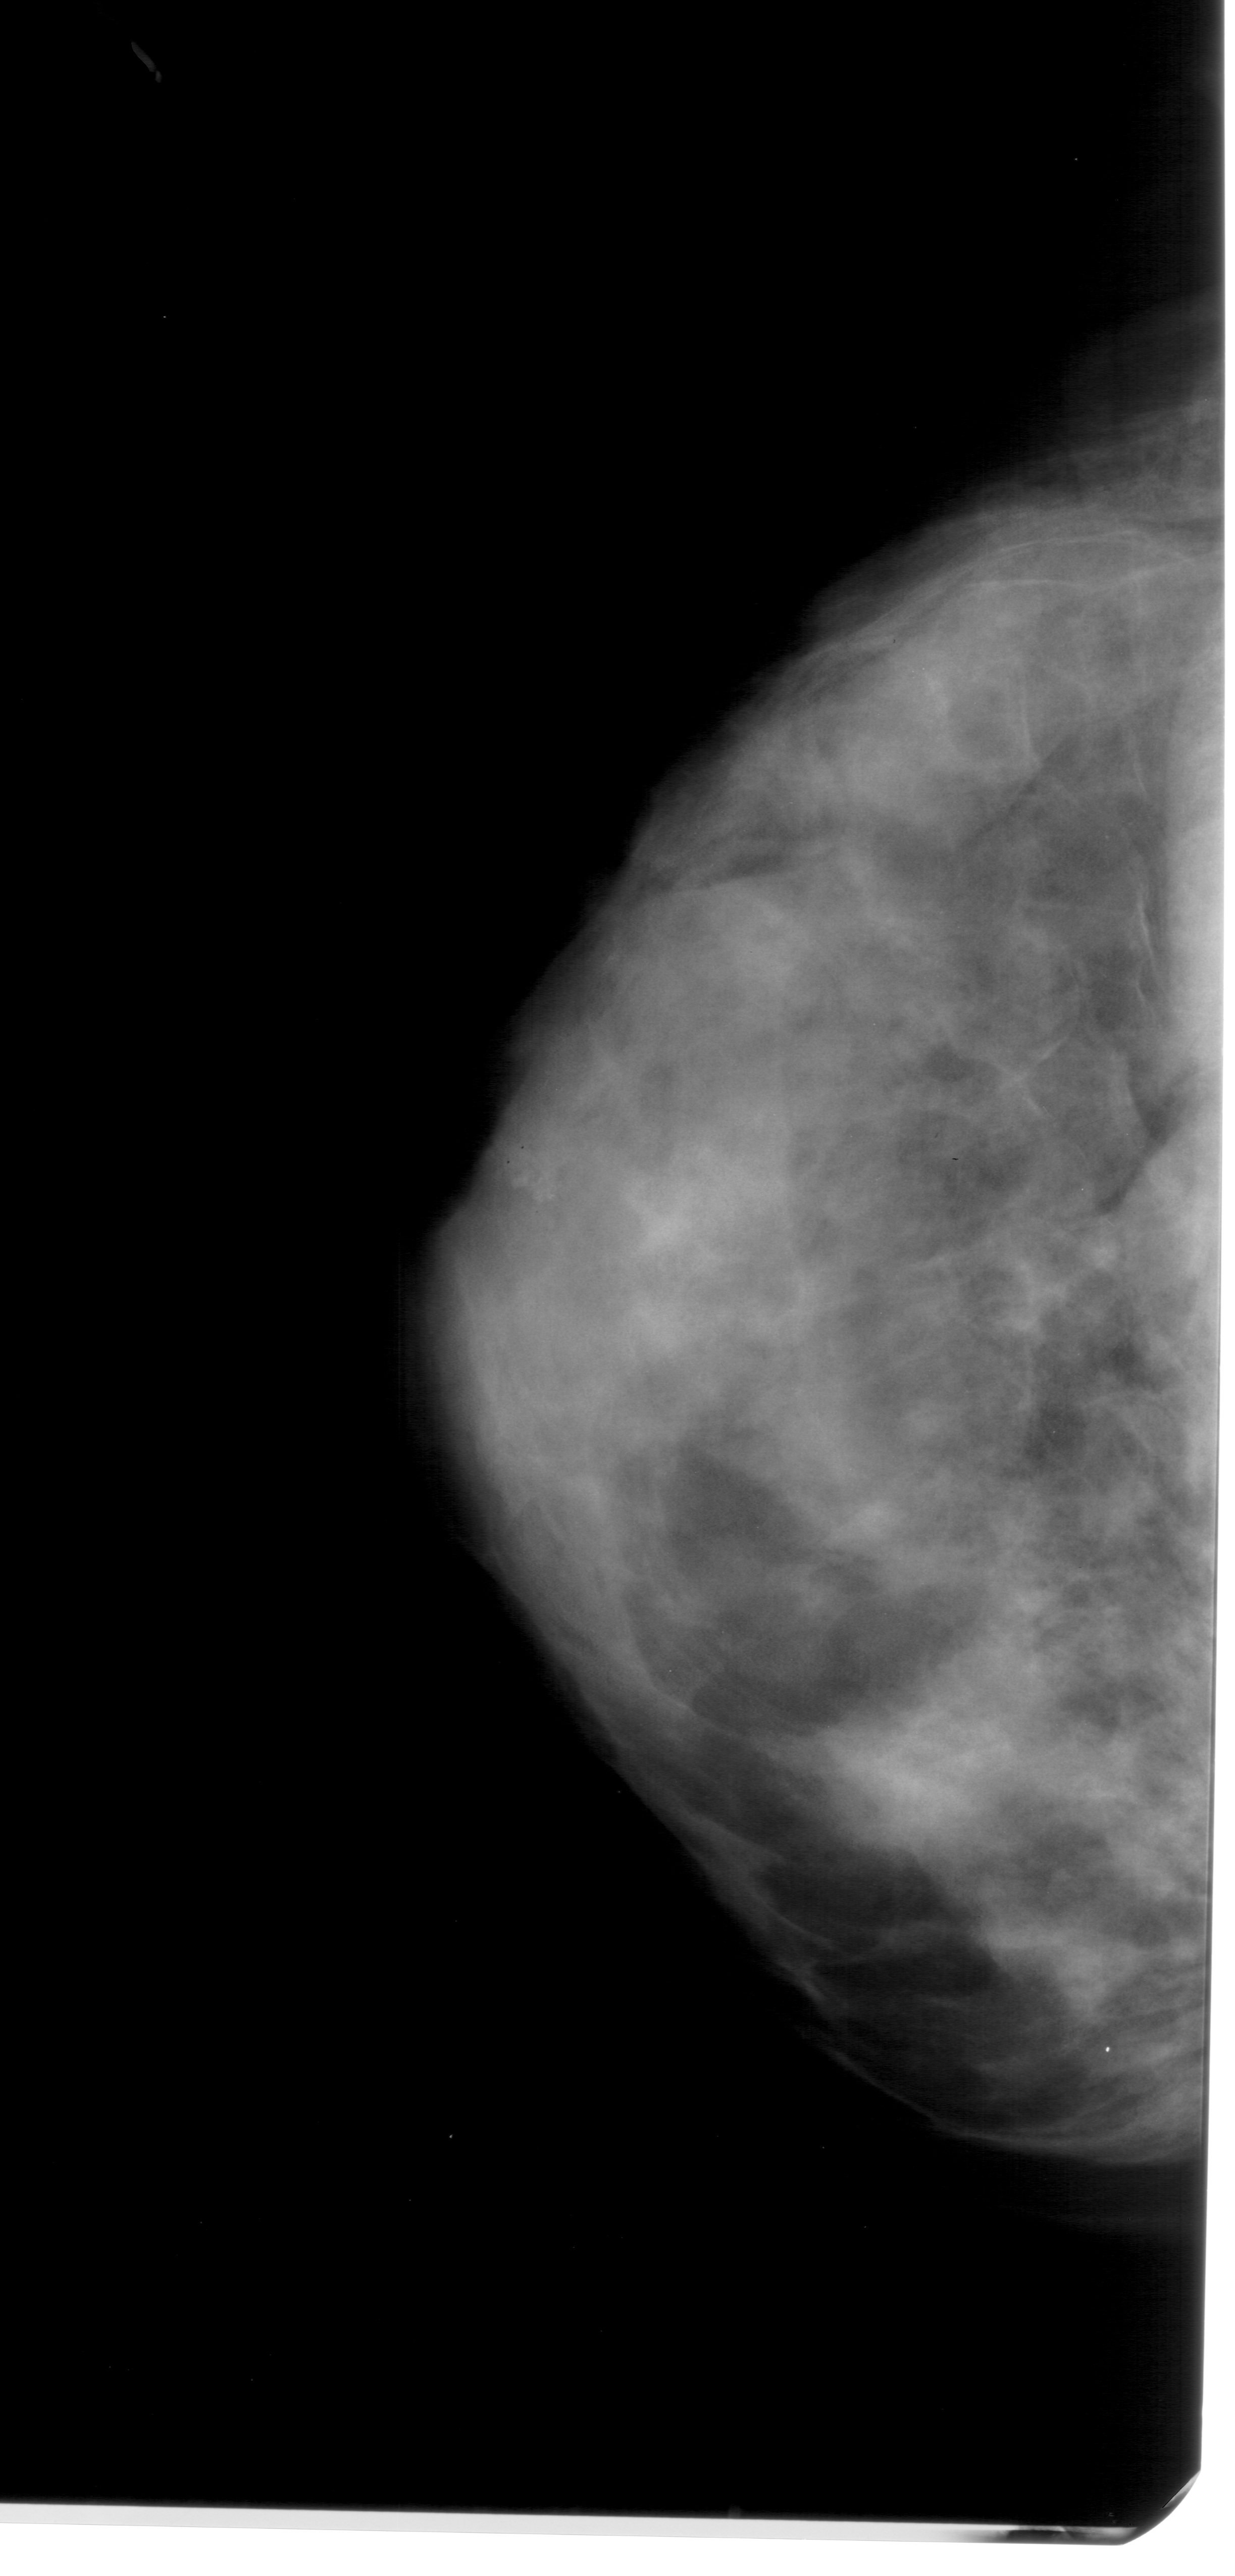
Scanned film-screen mammogram; left breast; CC view; breast composition: extremely dense (BI-RADS density category 4 of 4).
- Marked abnormality: calcifications, morphology pleomorphic, distribution clustered; BI-RADS assessment category 4; pathology result (as recorded, not read from the image): benign.